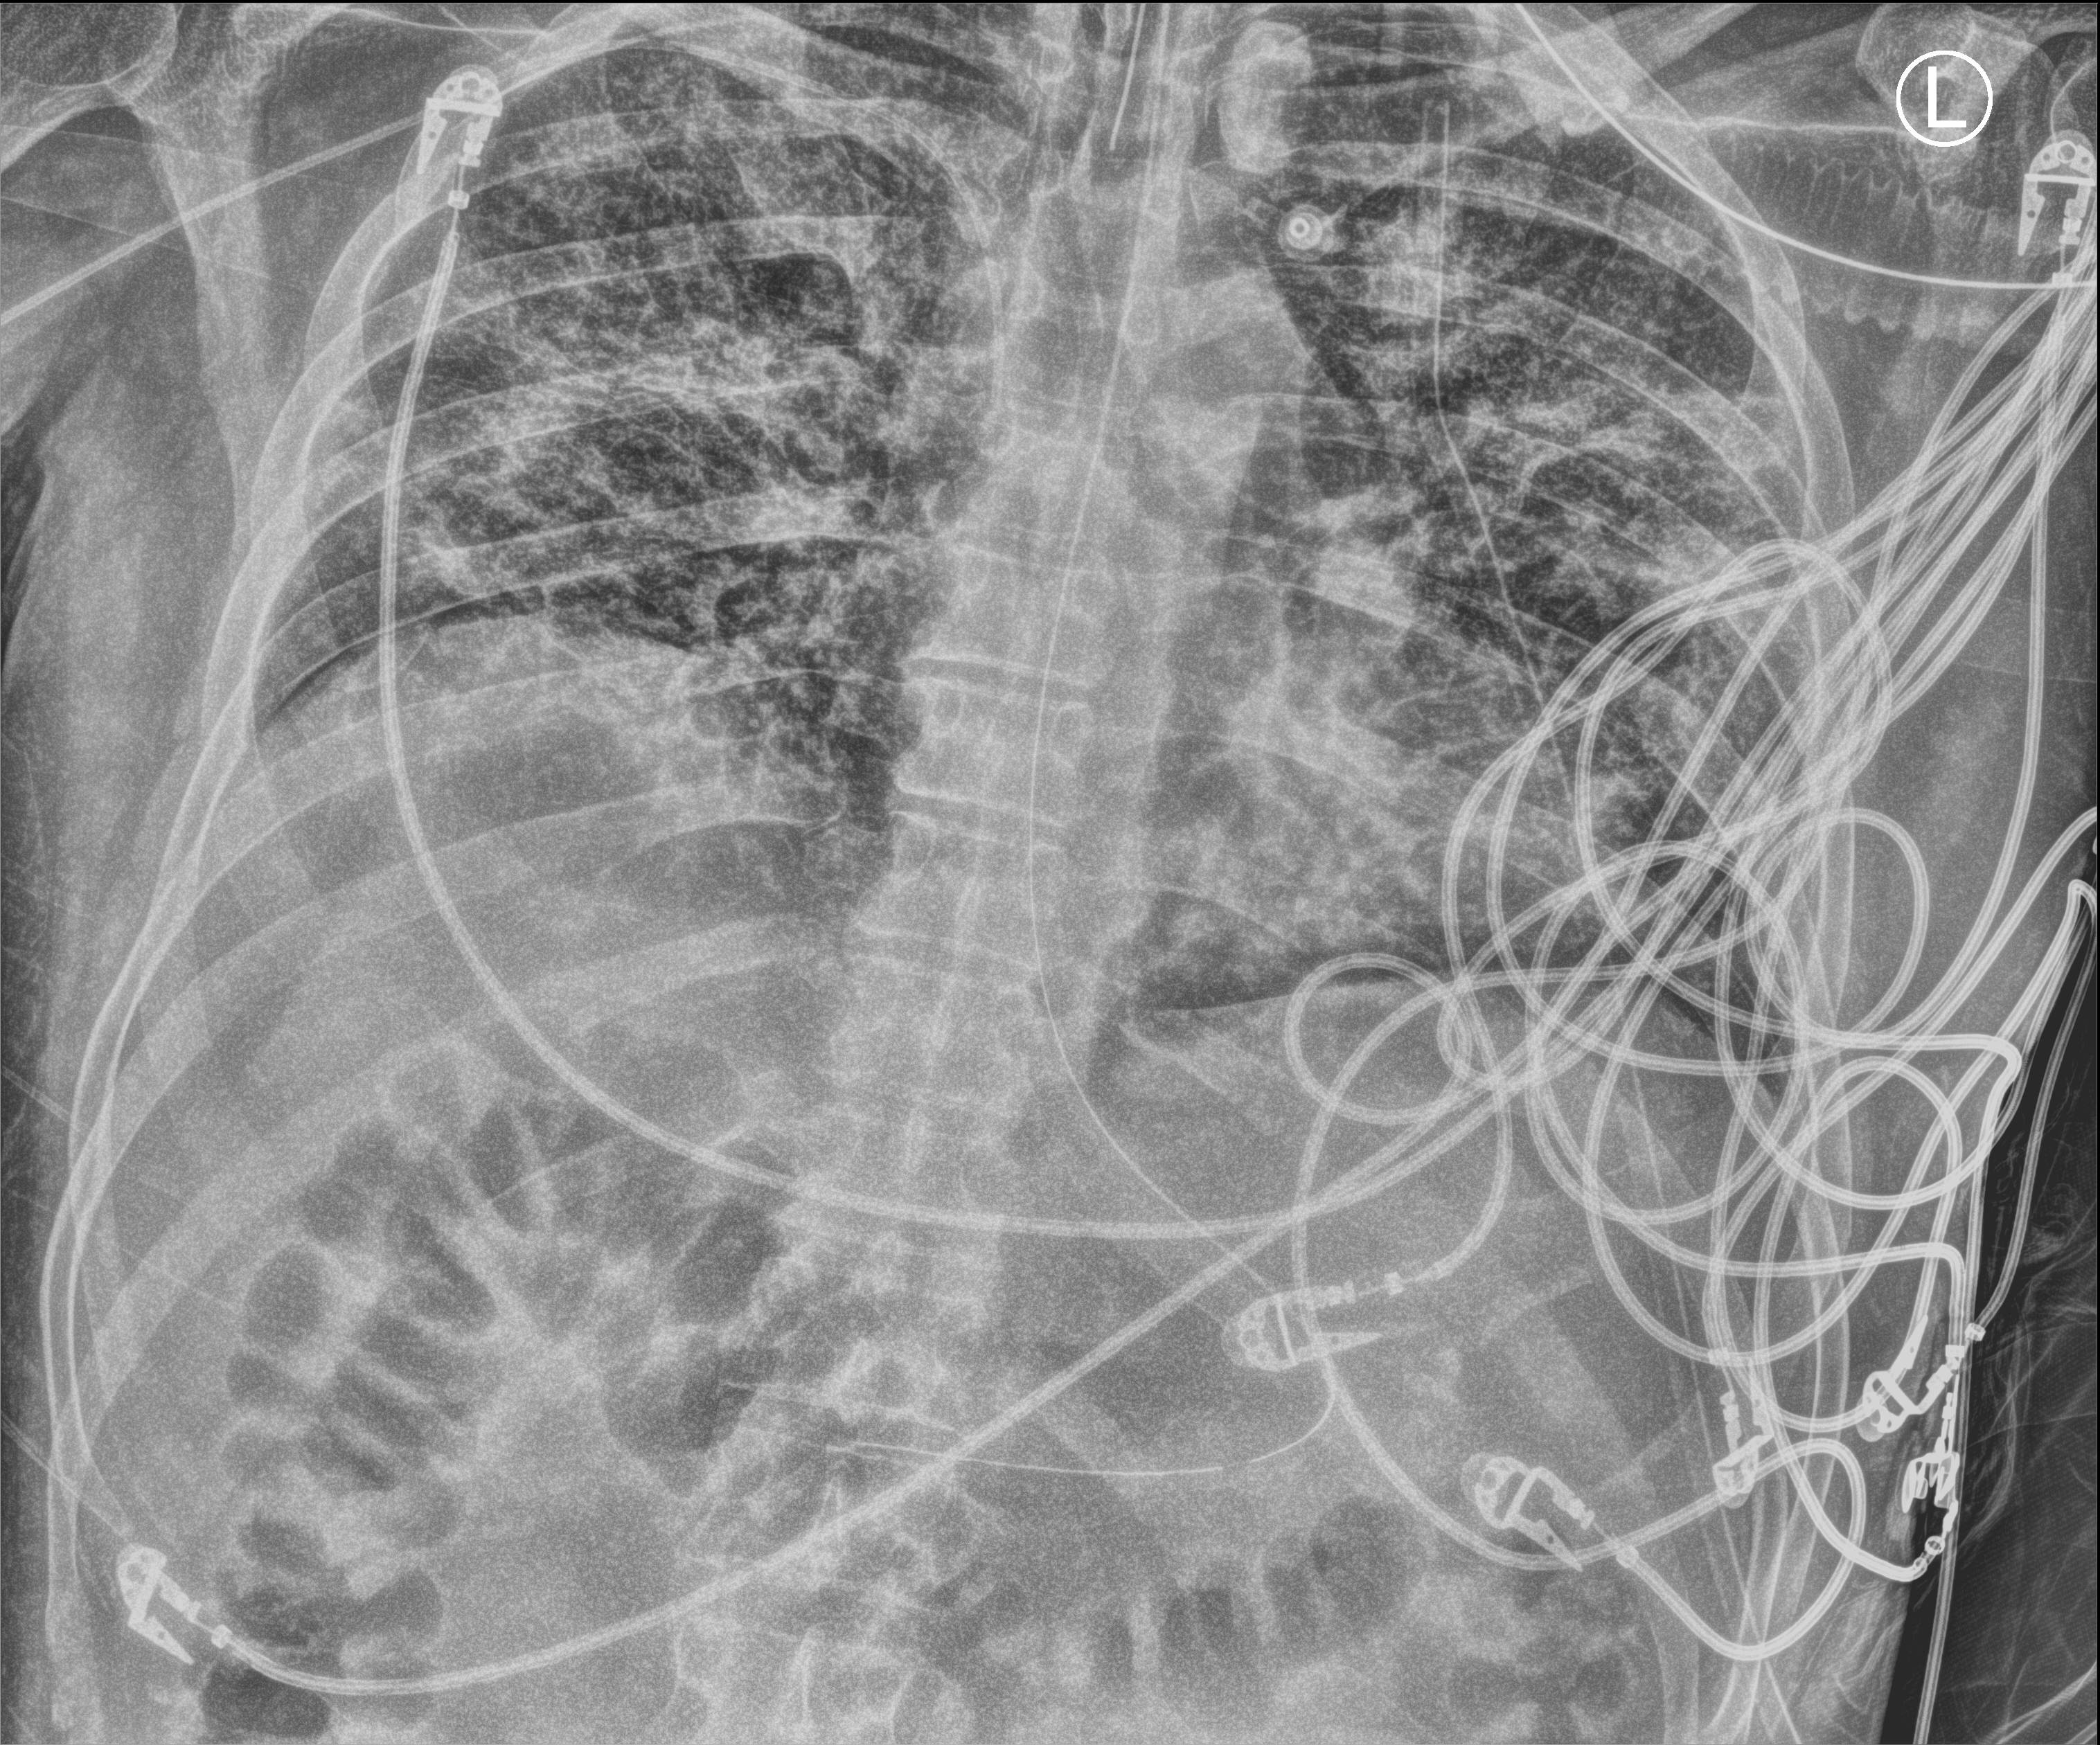
Chest X-ray (portable), anteroposterior (AP) projection. Male patient hospitalised with COVID-19, age 18–59 years.
From the hospital-stay record, not from the radiograph (when in the stay this image was taken is not recorded): mechanically ventilated during this hospital stay: yes; chronic kidney disease (admission record): no; smoking status (admission record): never.